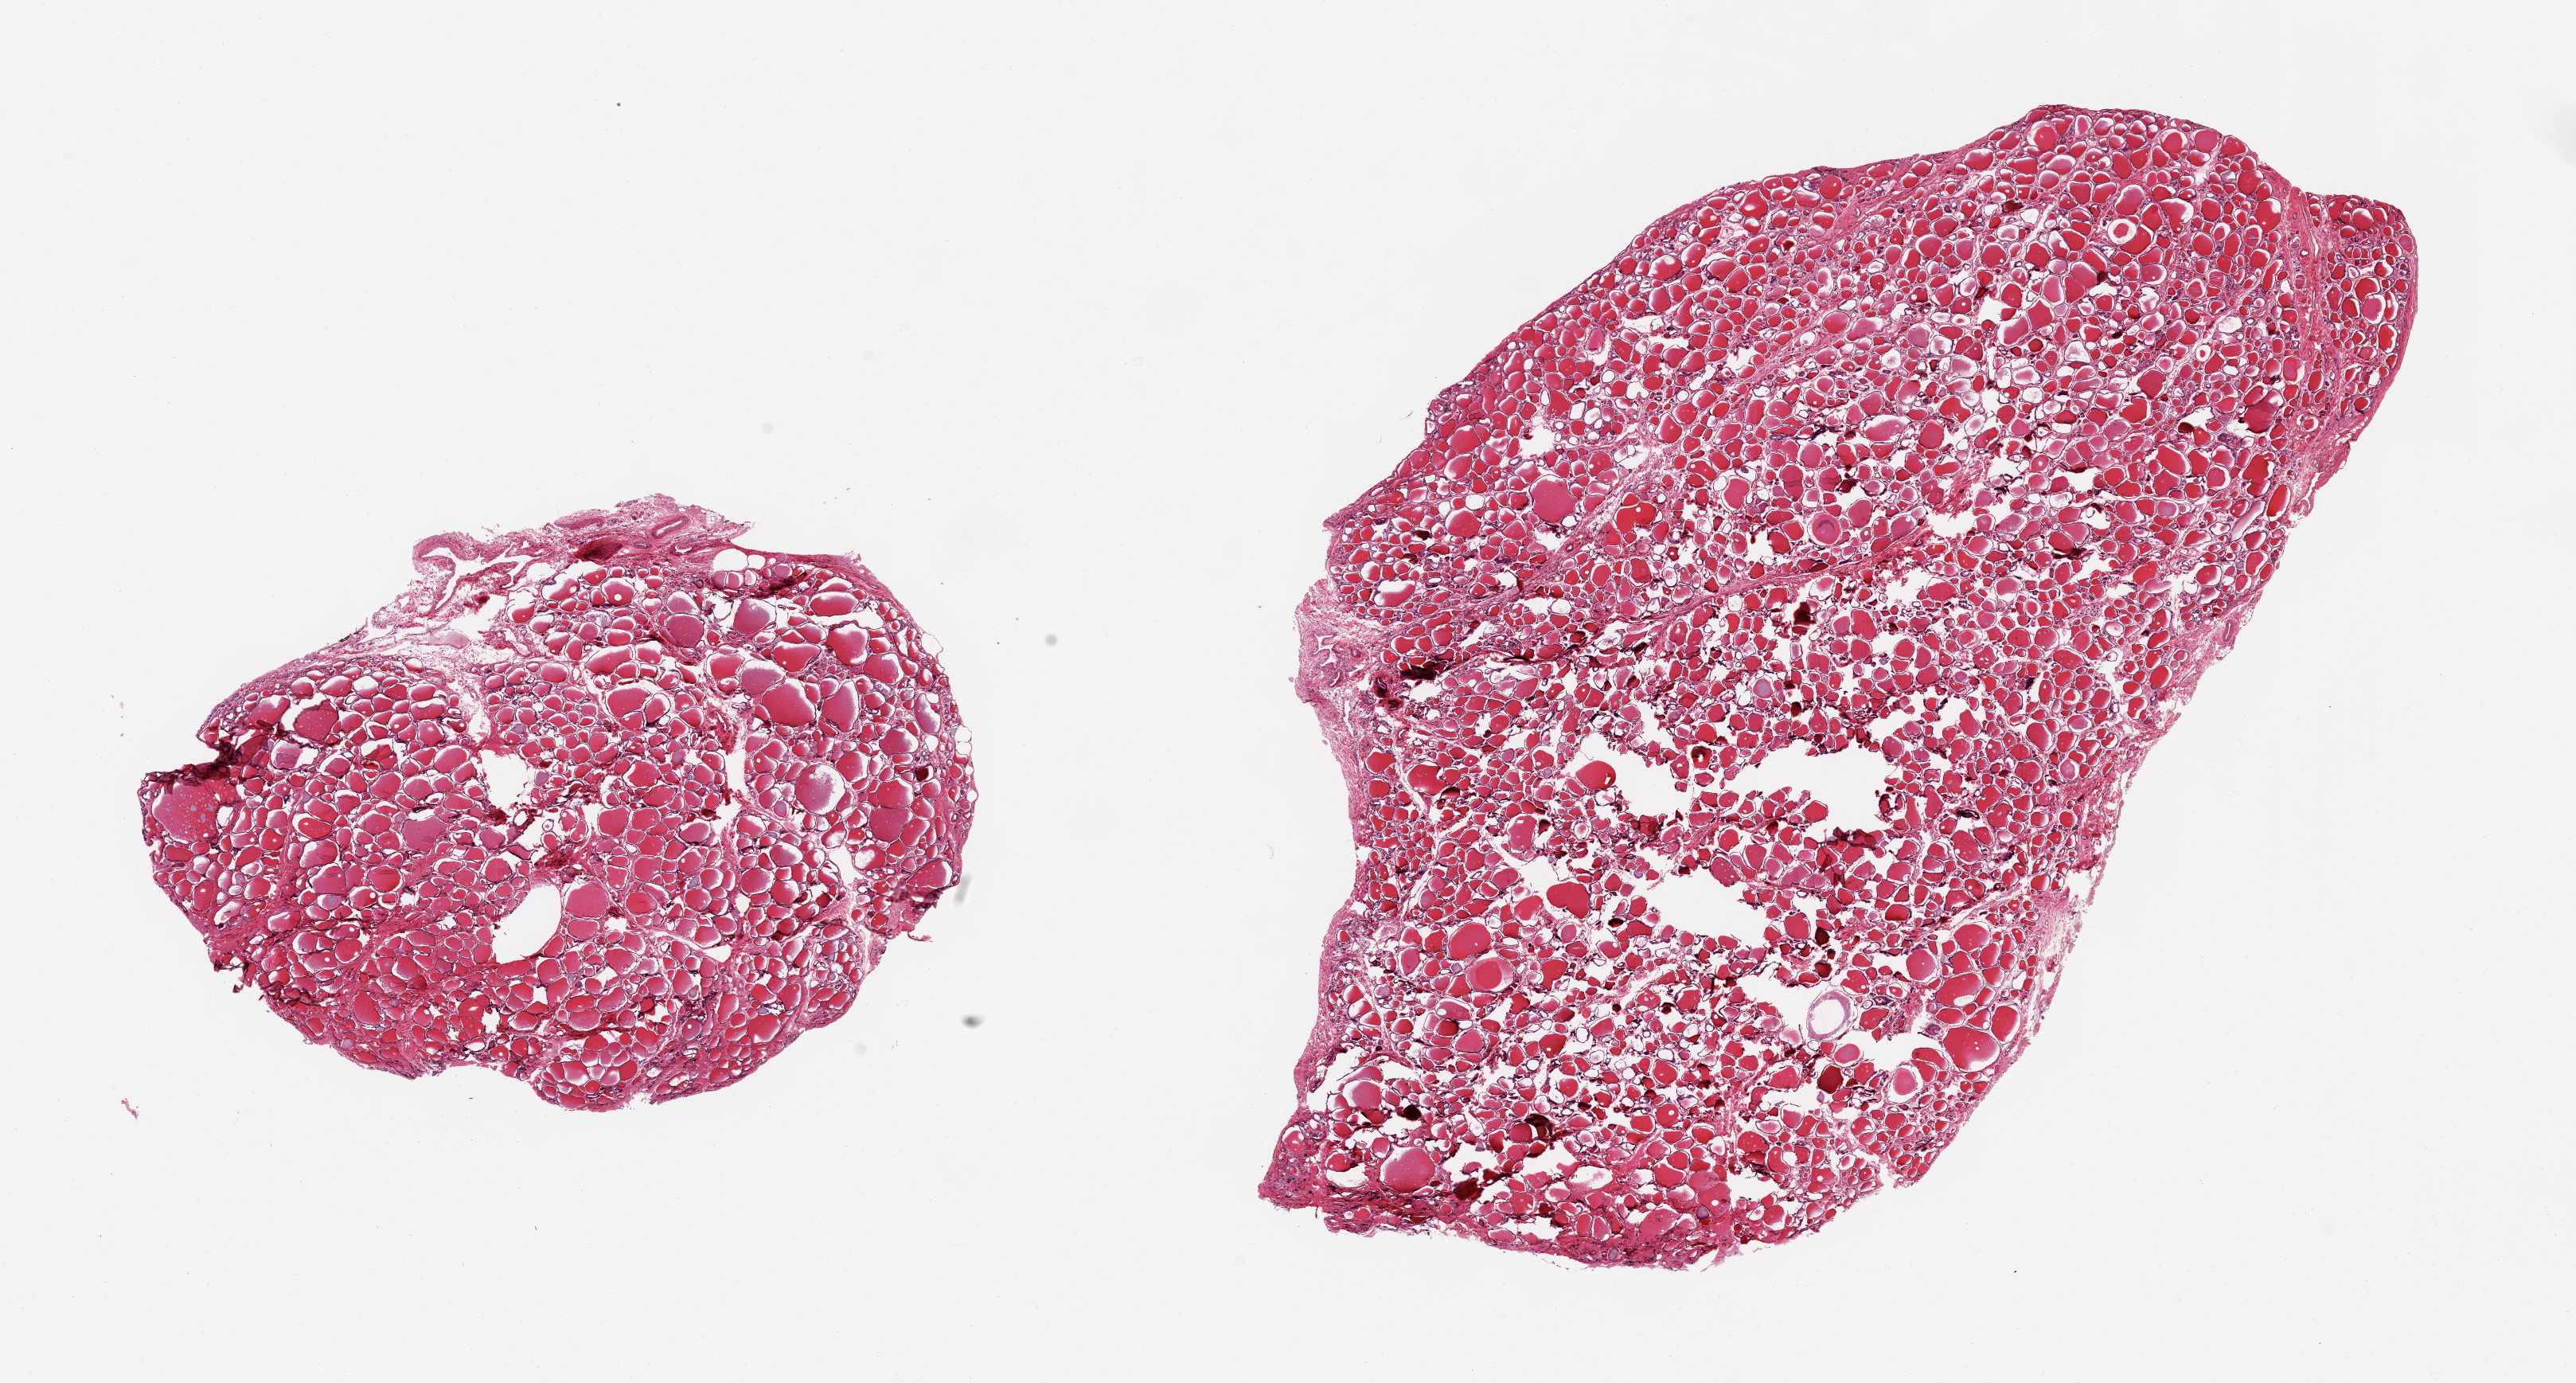
Whole-slide image, haematoxylin and eosin stain, brightfield — shown as a low-resolution overview of the whole scanned area (about 25.6 x 13.7 mm, slide scanned at 20x), PAXgene-fixed paraffin-embedded (PFPE) section, sampled site (target tissue): thyroid, tissue donor sample. Donor sex: female.
- reviewer comment on this tissue sample: 2 pieces